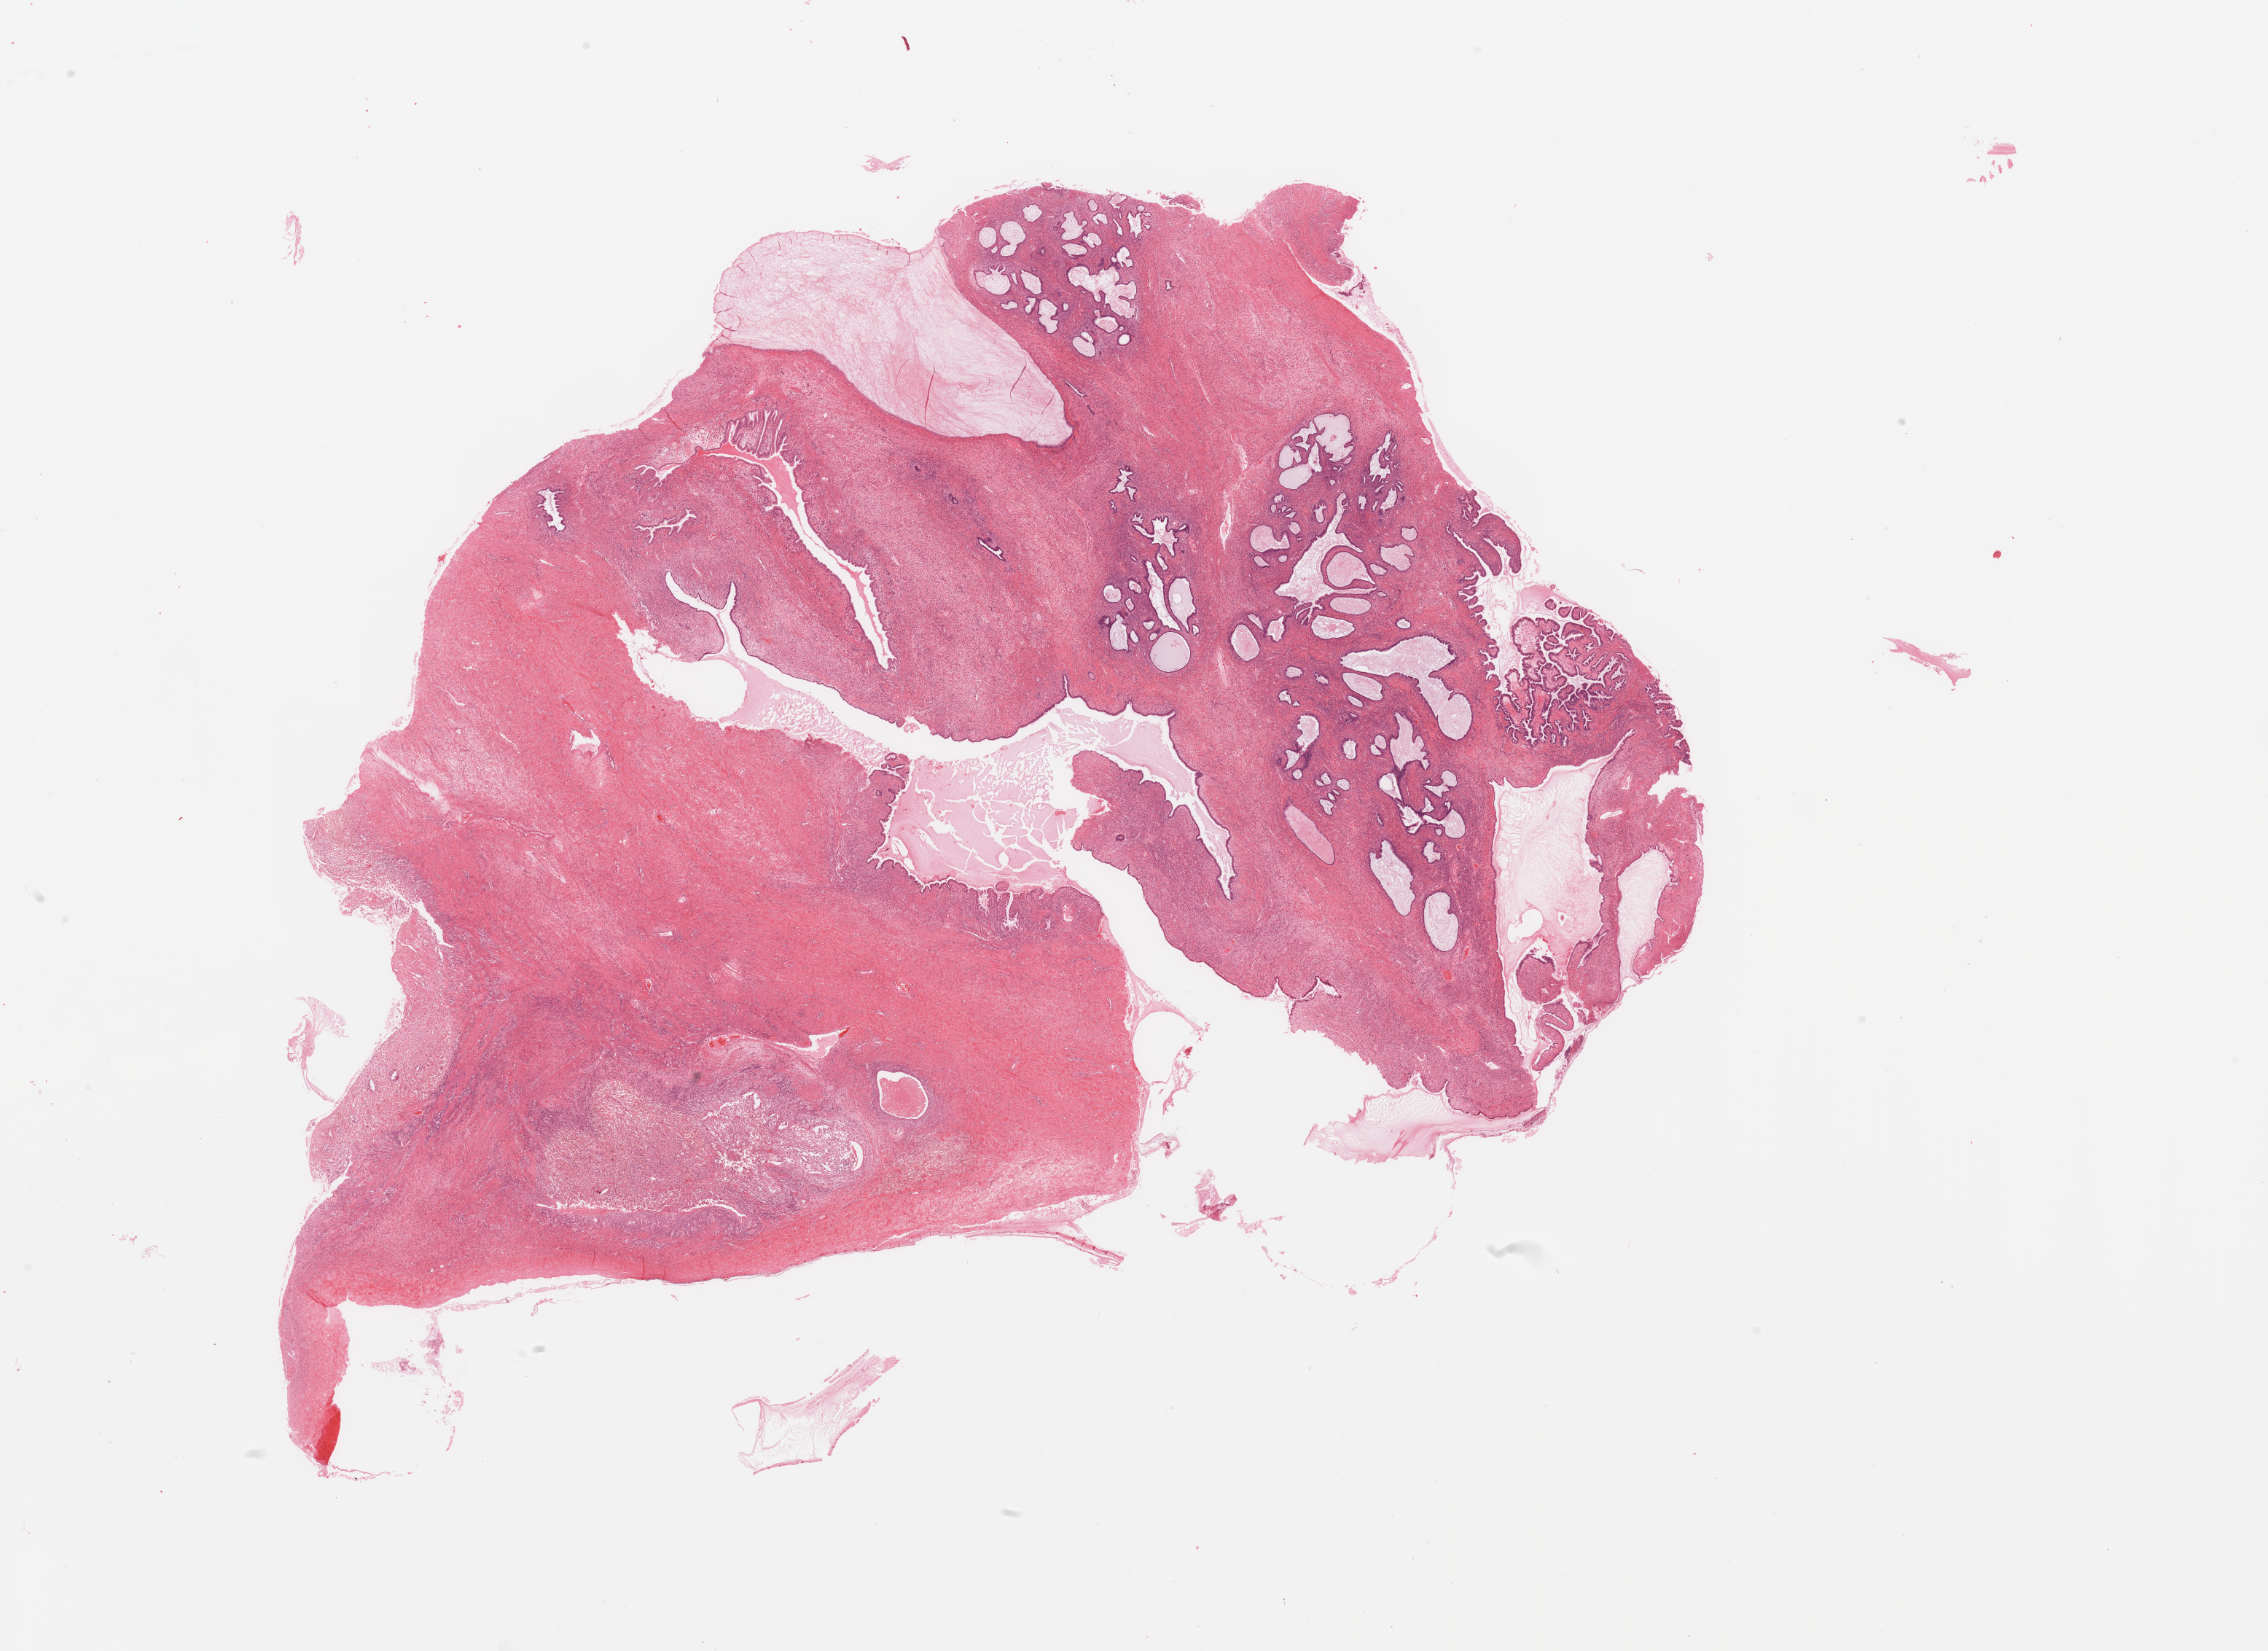
Whole-slide histology image, Hematoxylin and eosin (H&E) stained — a low-resolution overview of the entire scanned area, about 24.6 x 17.9 mm (from a 20x scan). Lung, normal (non-tumour) tissue. 56-year-old male patient.
This section: normal (non-tumour) tissue from the same patient. Patient diagnosis: Adenocarcinoma, NOS.